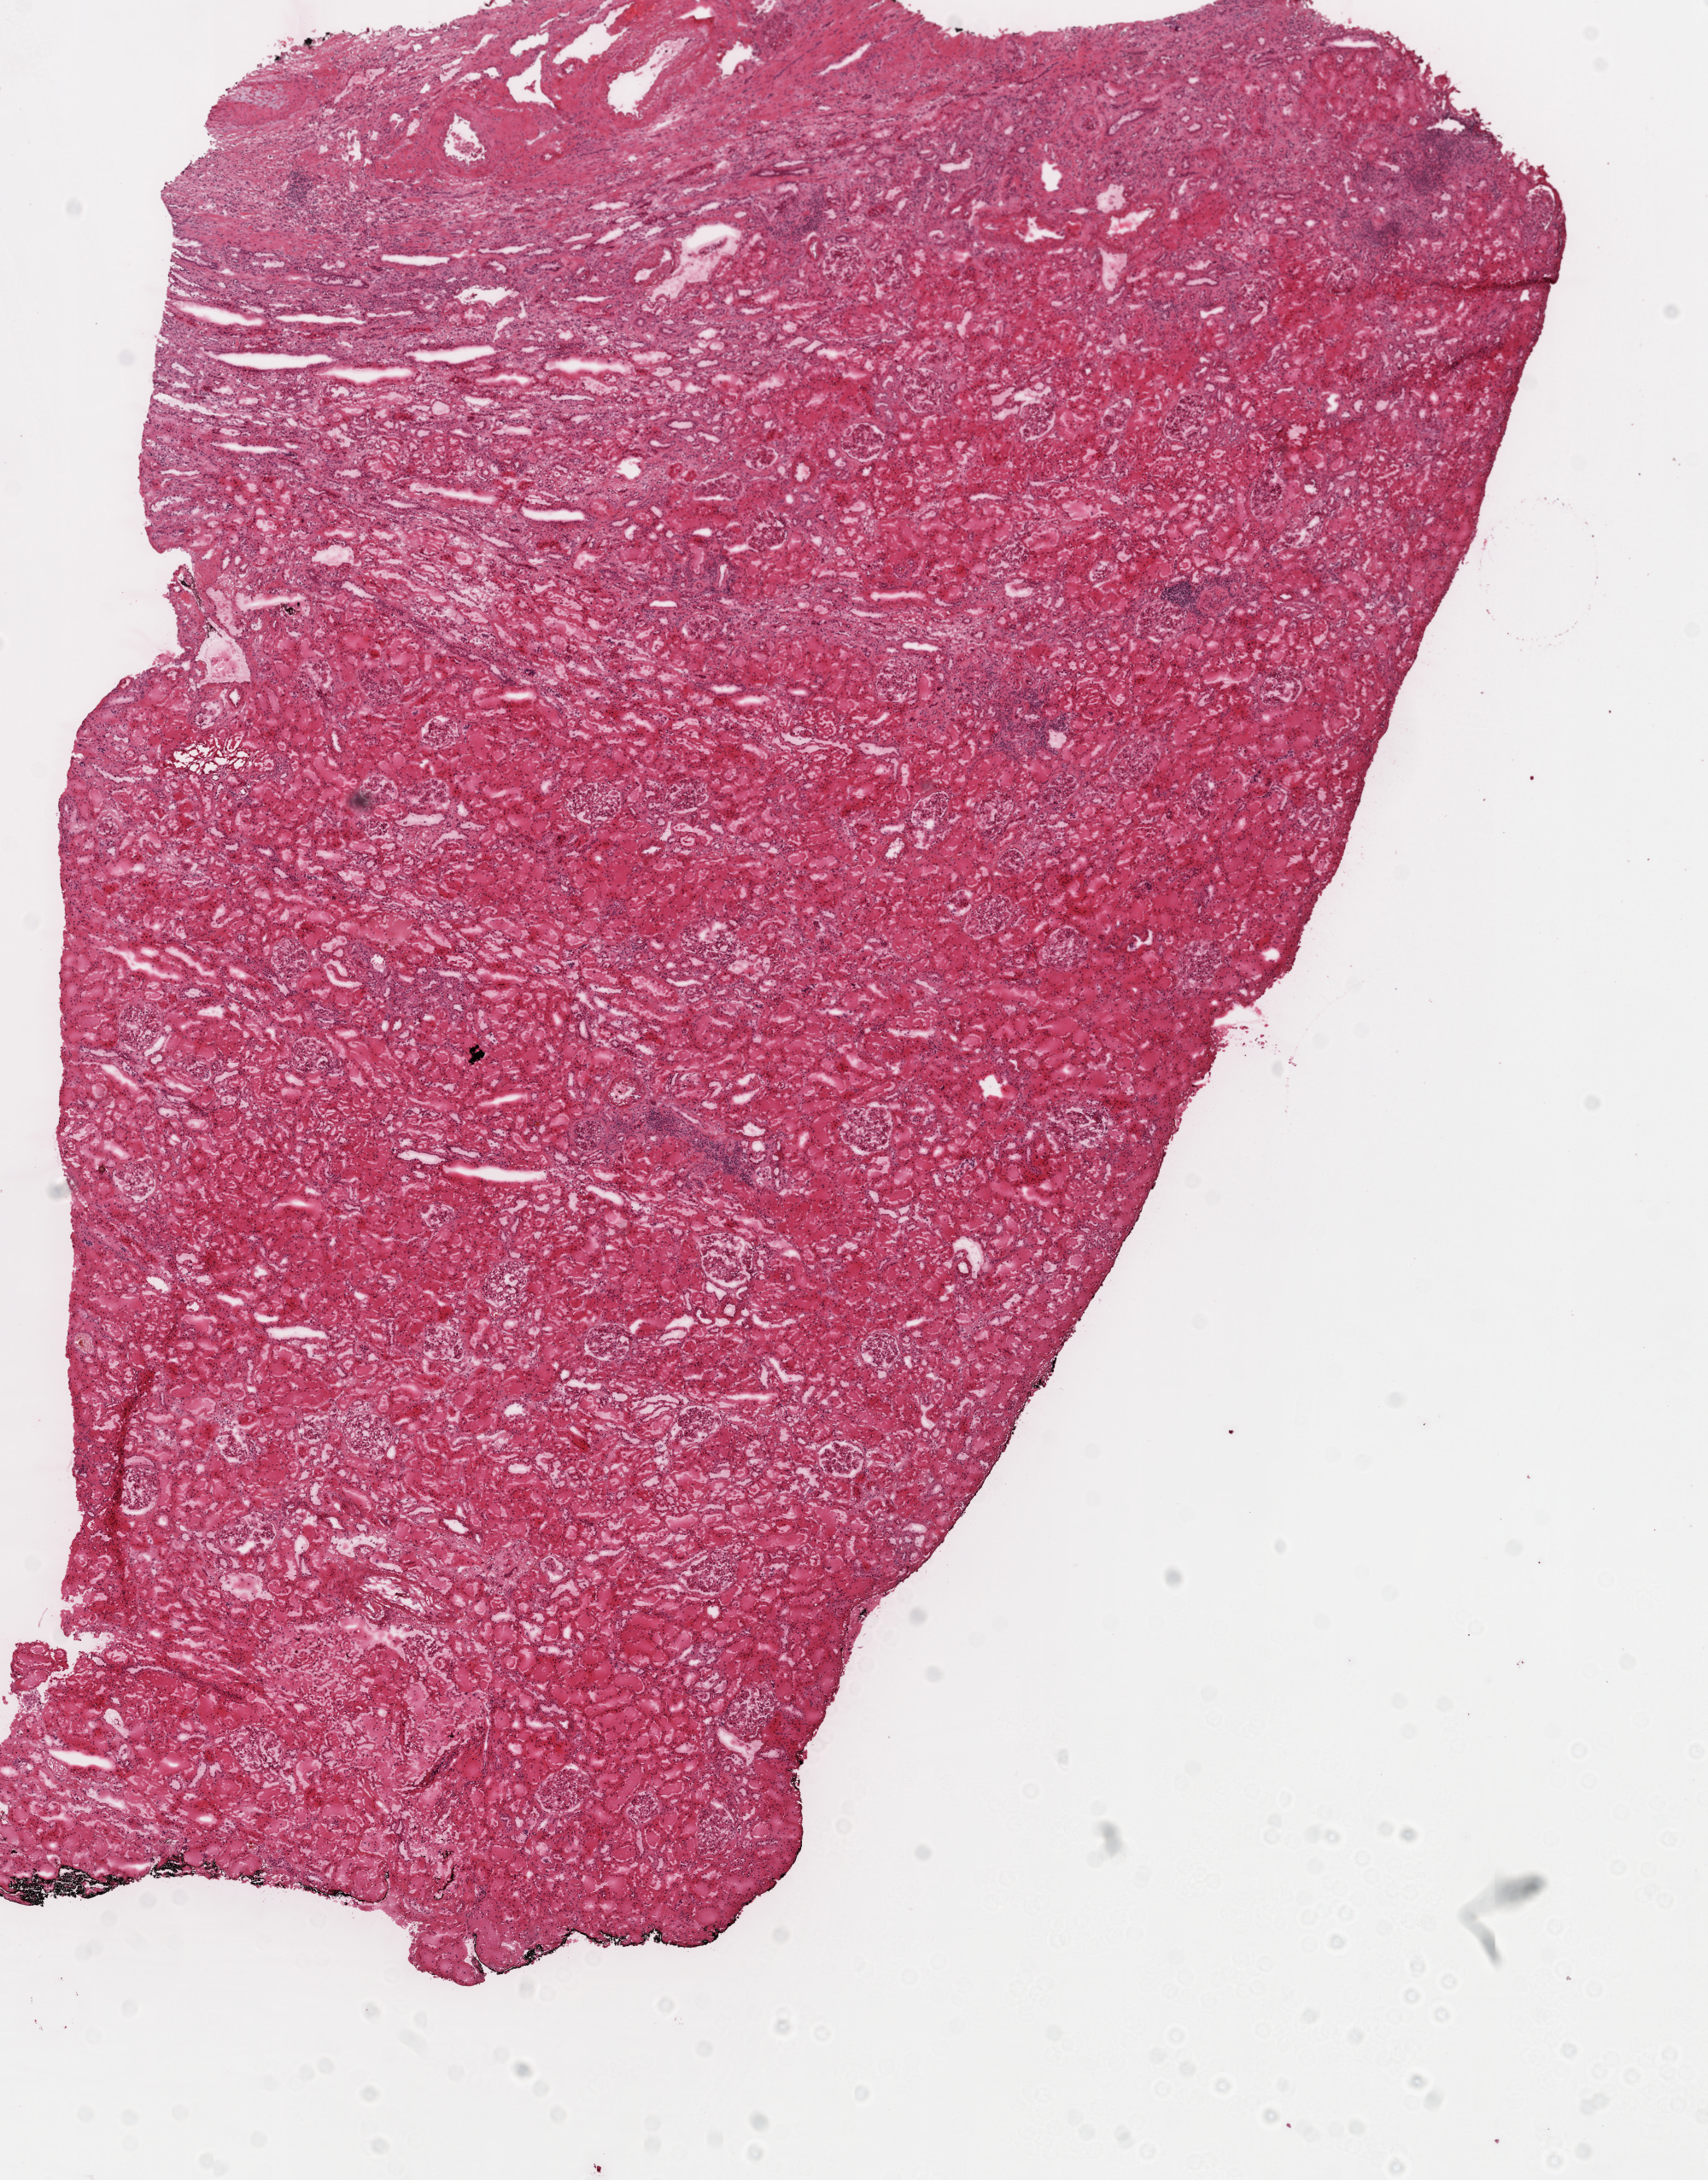
Digitized H&E-stained tissue section (whole slide), shown as a low-resolution overview of the whole scanned area (about 8.0 x 10.2 mm, slide scanned at 20x), frozen section, kidney, solid tissue normal (non-tumour tissue) sample. Patient: male, age at initial diagnosis 77 years.
This section: solid tissue normal (non-tumour) sample from the same patient. Patient diagnosis: Clear cell adenocarcinoma, NOS.